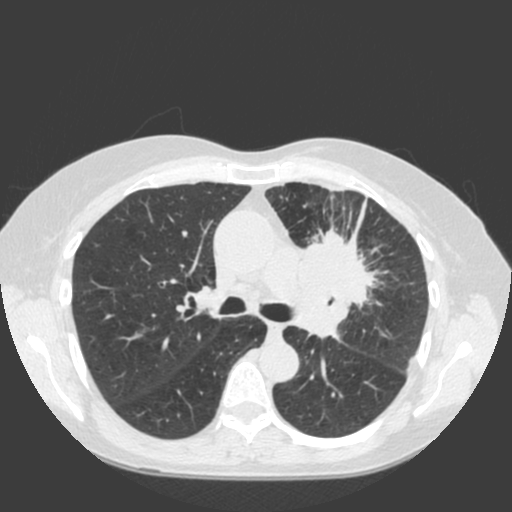
Low-dose screening chest CT, one axial slice; position 121 of 184 along the scan axis; lung window (W 1500 / L -600 HU); 2 mm slice thickness; 512 × 512 image matrix, field of view 350 × 350 mm.
Annotated regions visible in this slice (expert manual segmentation):
- lesion 1 (tumor, hilum of left lung): bounding box (x1, y1, x2, y2) in pixels: (291, 231, 380, 337)